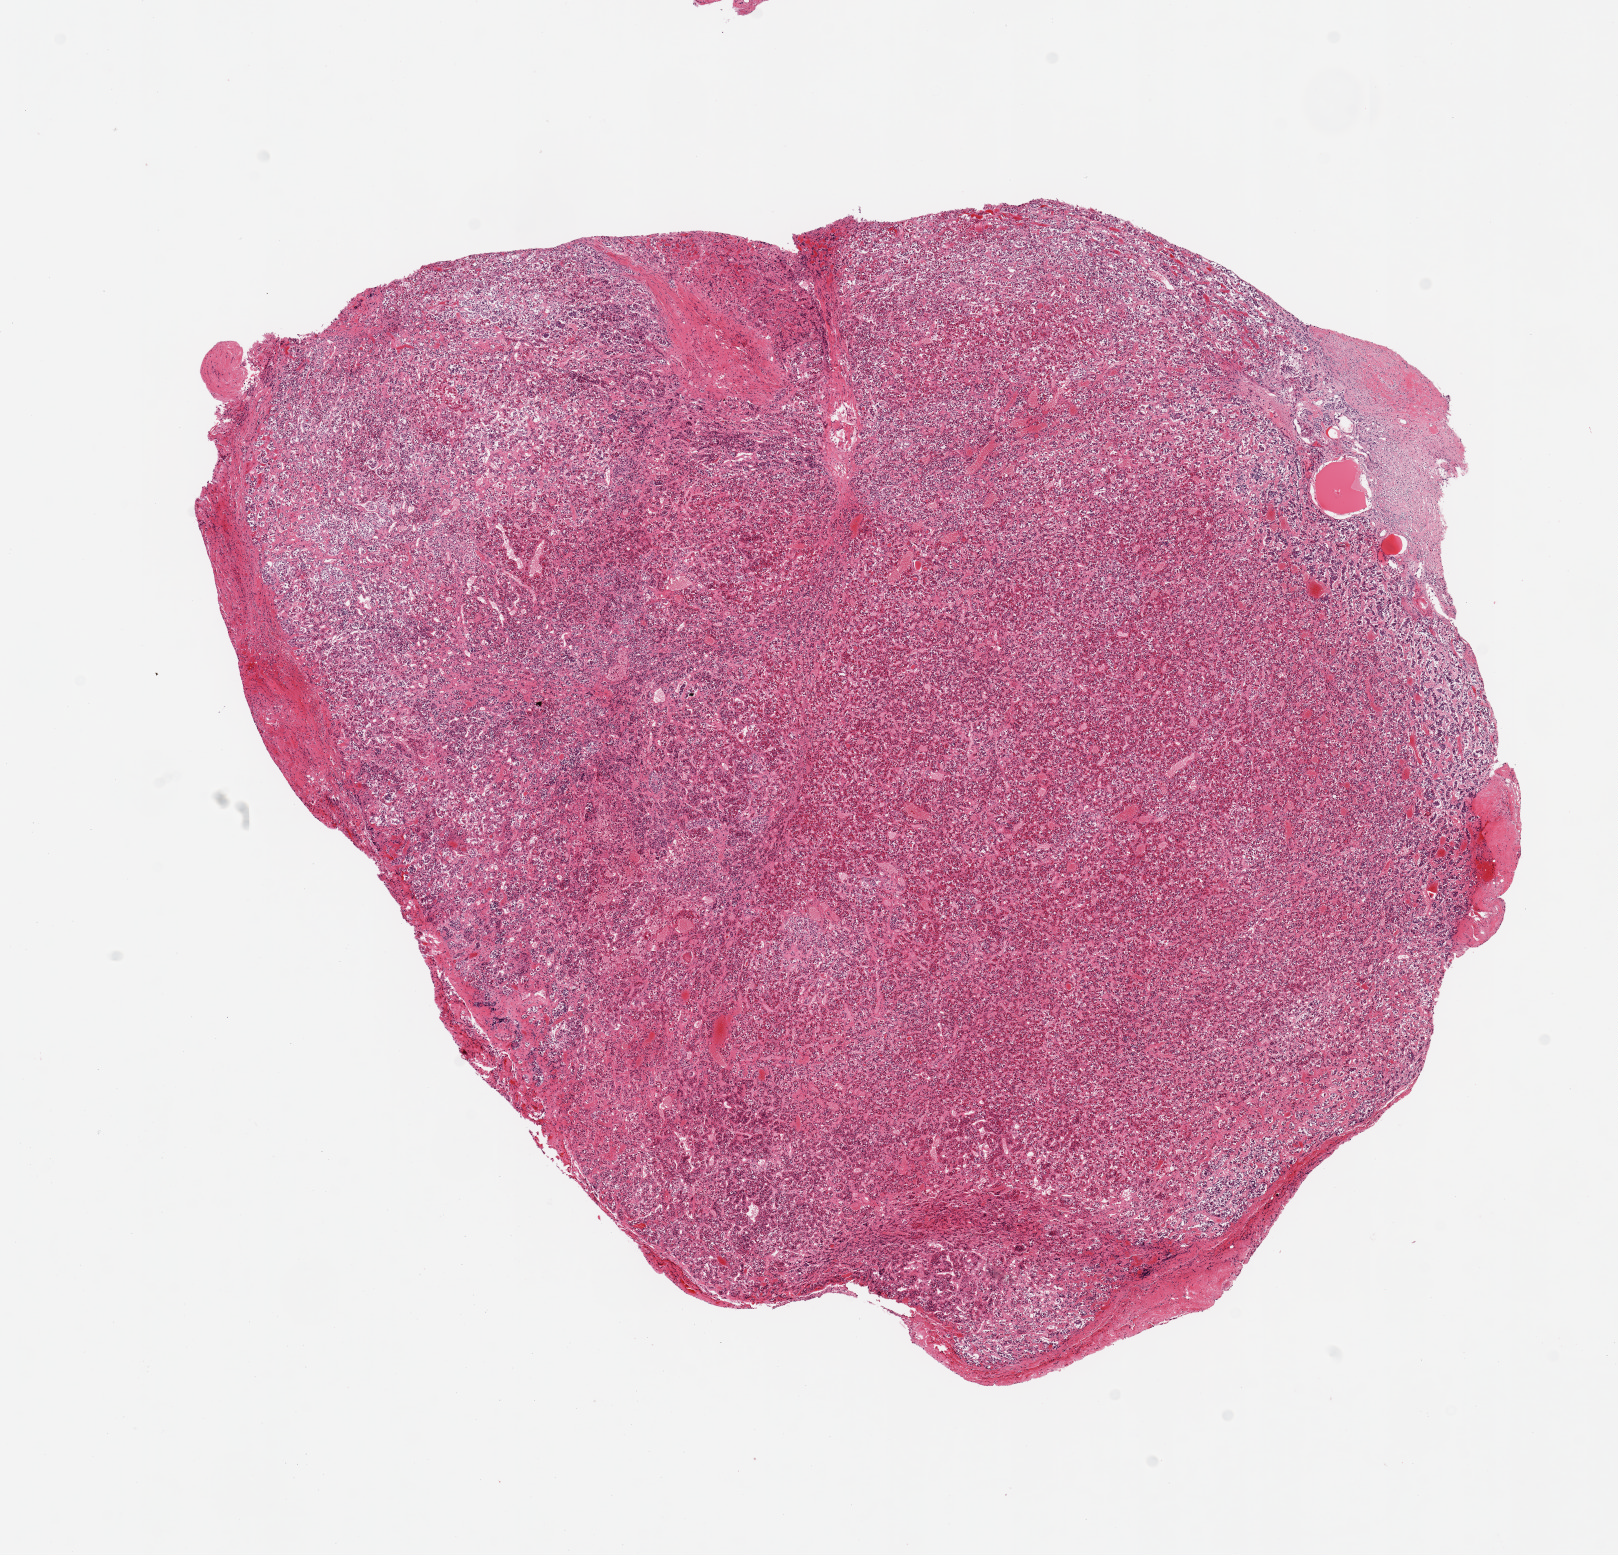
Haematoxylin and eosin whole-slide image, low-resolution overview of the scanned area, about 12.8 x 12.3 mm. PAXgene-fixed paraffin-embedded (PFPE) section. Target tissue: pituitary. Donor tissue sample. Donor sex: female.
Pathologist's review note for this sample: 1 piece, all adenohypophysis.